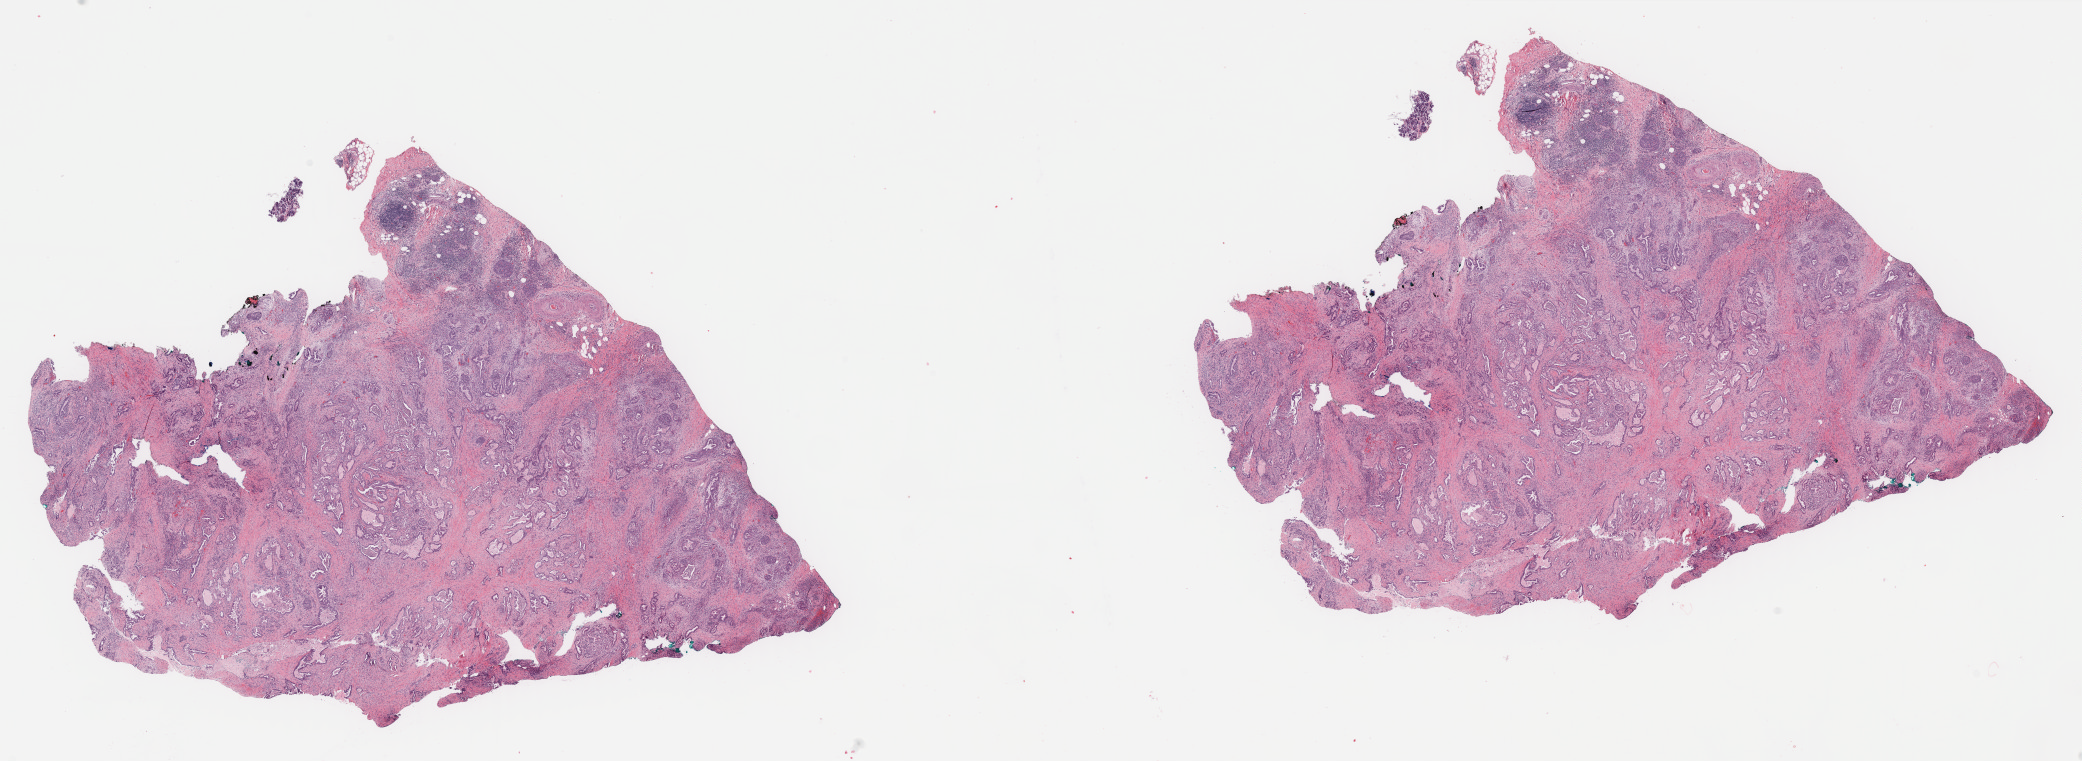
Digitized H&E tissue section (whole slide), a low-resolution overview of the entire scanned area, about 32.9 x 12.0 mm (slide scanned at 40x); FFPE section; primary tumour sample from the pancreas. Male patient; age at initial diagnosis 65 years. Histologic grade: G2 (moderately differentiated).
Histologic diagnosis: Adenocarcinoma, NOS (head of pancreas). Lymph nodes positive (case pathology): 0 of 8 examined. AJCC pathologic stage: IIA (7th edition).